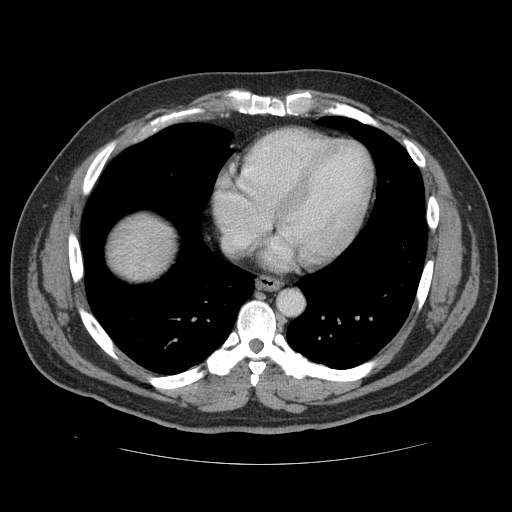
Contrast-enhanced abdominal CT (liver protocol), one axial slice; slice 111 of 113 in the series (ordered by position); 120 kVp; soft-tissue window (W 400 / L 40 HU); 2.5 mm slice thickness; 512 × 512 image matrix, field of view 400 × 400 mm. From the clinical record (not read from this slice): diagnosis: hepatocellular carcinoma (patient treated with transarterial chemoembolisation; whether this scan precedes or follows treatment is not stated here); TNM stage (as recorded): Stage-II; Child-Pugh class: B; tumour nodularity: multinodular.
Annotated regions visible in this slice (semi-automatically segmented with operator editing):
- liver parenchyma outside the tumour (the mass and vessels are separate outlines, so this box may not span the whole liver): bounding box (x1, y1, x2, y2) in pixels: (112, 218, 166, 270)